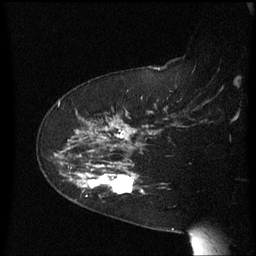
Breast MRI (dynamic contrast-enhanced), one sagittal slice; dynamic contrast-enhanced series, image 2 of 3 at this slice position (ordered by acquisition); 1.5 T; TE 4.2 ms, TR 8.4 ms; 256 × 256 image matrix, field of view 200 × 200 mm. Female patient, age 63 years. Case-level facts recorded for this patient, not image findings: setting: breast cancer imaged before/during neoadjuvant chemotherapy; receptor status: HER2-positive.
Outlined on this slice (semi-automatic segmentation, software-assisted and operator-edited):
- analysis volume of interest (the breast-tissue region the enhancement analysis was run in; not a lesion): bounding box <63,144,147,205> (left, top, right, bottom; pixels)
- tumour enhancement mask (voxels above the 70 % enhancement threshold inside the analysis volume of interest): <70,165,138,194>